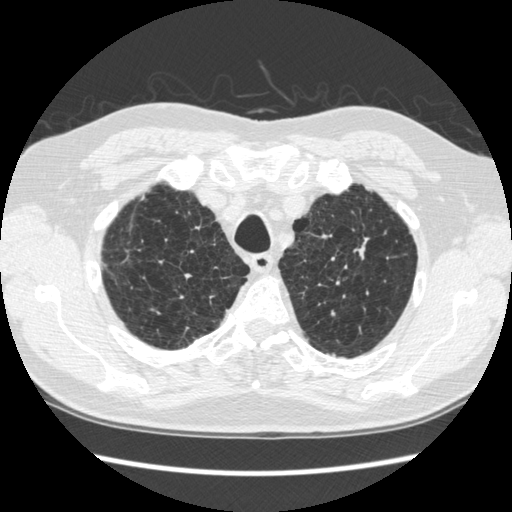
Low-dose screening chest CT, axial slice; second screening round (one year after baseline); lung window (W 1500 / L -600 HU); 1.25 mm slice thickness; standard (soft-tissue) reconstruction kernel (STANDARD); 120 kVp; 512 × 512 image matrix. Male participant, aged 70 years at enrolment. Former smoker at enrolment.
Expert reader's lesion annotation, box from (x=333, y=214) to (x=394, y=281) px. The screening reader recorded 5 non-calcified nodules or masses ≥4 mm on this exam; which of them this box marks is not recorded. Lung cancer was diagnosed 479 days after this screen: squamous cell carcinoma, NOS, left upper lobe, moderately differentiated (G2), stage IA (AJCC 6th edition), 18 mm at pathology.